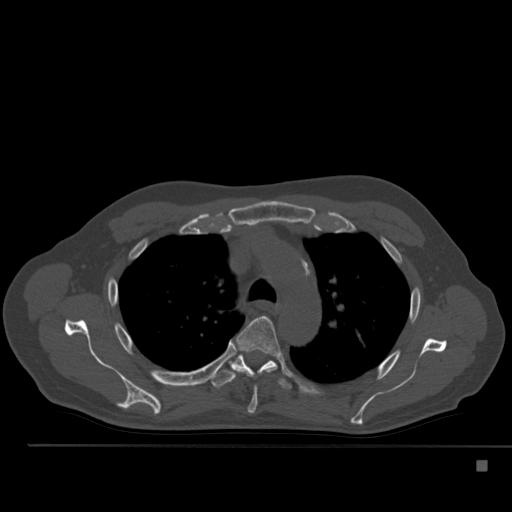
CT including the spine, one axial slice; position 375 of 517 along the scan axis; reconstruction kernel Br40s; bone window (W 1800 / L 400 HU); 1.5 mm slice thickness; 512 × 512 image matrix, field of view 408 × 408 mm. Patient: male, 70 years. From the clinical record (not read from this slice): primary cancer: renal; vertebrae with lytic lesions (as recorded): T4, T6, T10, T12, L3, L4, L5.
Annotated regions visible in this slice (semi-automatic segmentation, software-assisted and operator-edited):
- T4 vertebra: bounding box [x1, y1, x2, y2] px = [233, 316, 287, 414]
- T5 vertebra: [210, 354, 292, 390]